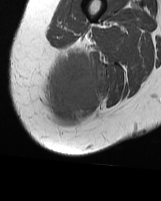
MRI of an extremity soft-tissue mass, one axial slice; position 16 of 70 along the scan axis; MR volume resampled by the dataset authors to the PET/CT grid (not the native acquisition matrix); 161 × 201 image matrix, field of view 157 × 196 mm. Female patient. From the clinical record (not read from this slice): histological type: synovial sarcoma; grade: intermediate; site of the primary tumour: right buttock.
Structures marked on this image (expert contour drawn on MRI and transferred to this co-registered scan by the dataset authors):
- gross tumour volume including surrounding oedema: bounding box (x1, y1, x2, y2) in pixels: (42, 47, 102, 121)
- gross tumour volume (mass): (47, 54, 102, 116)